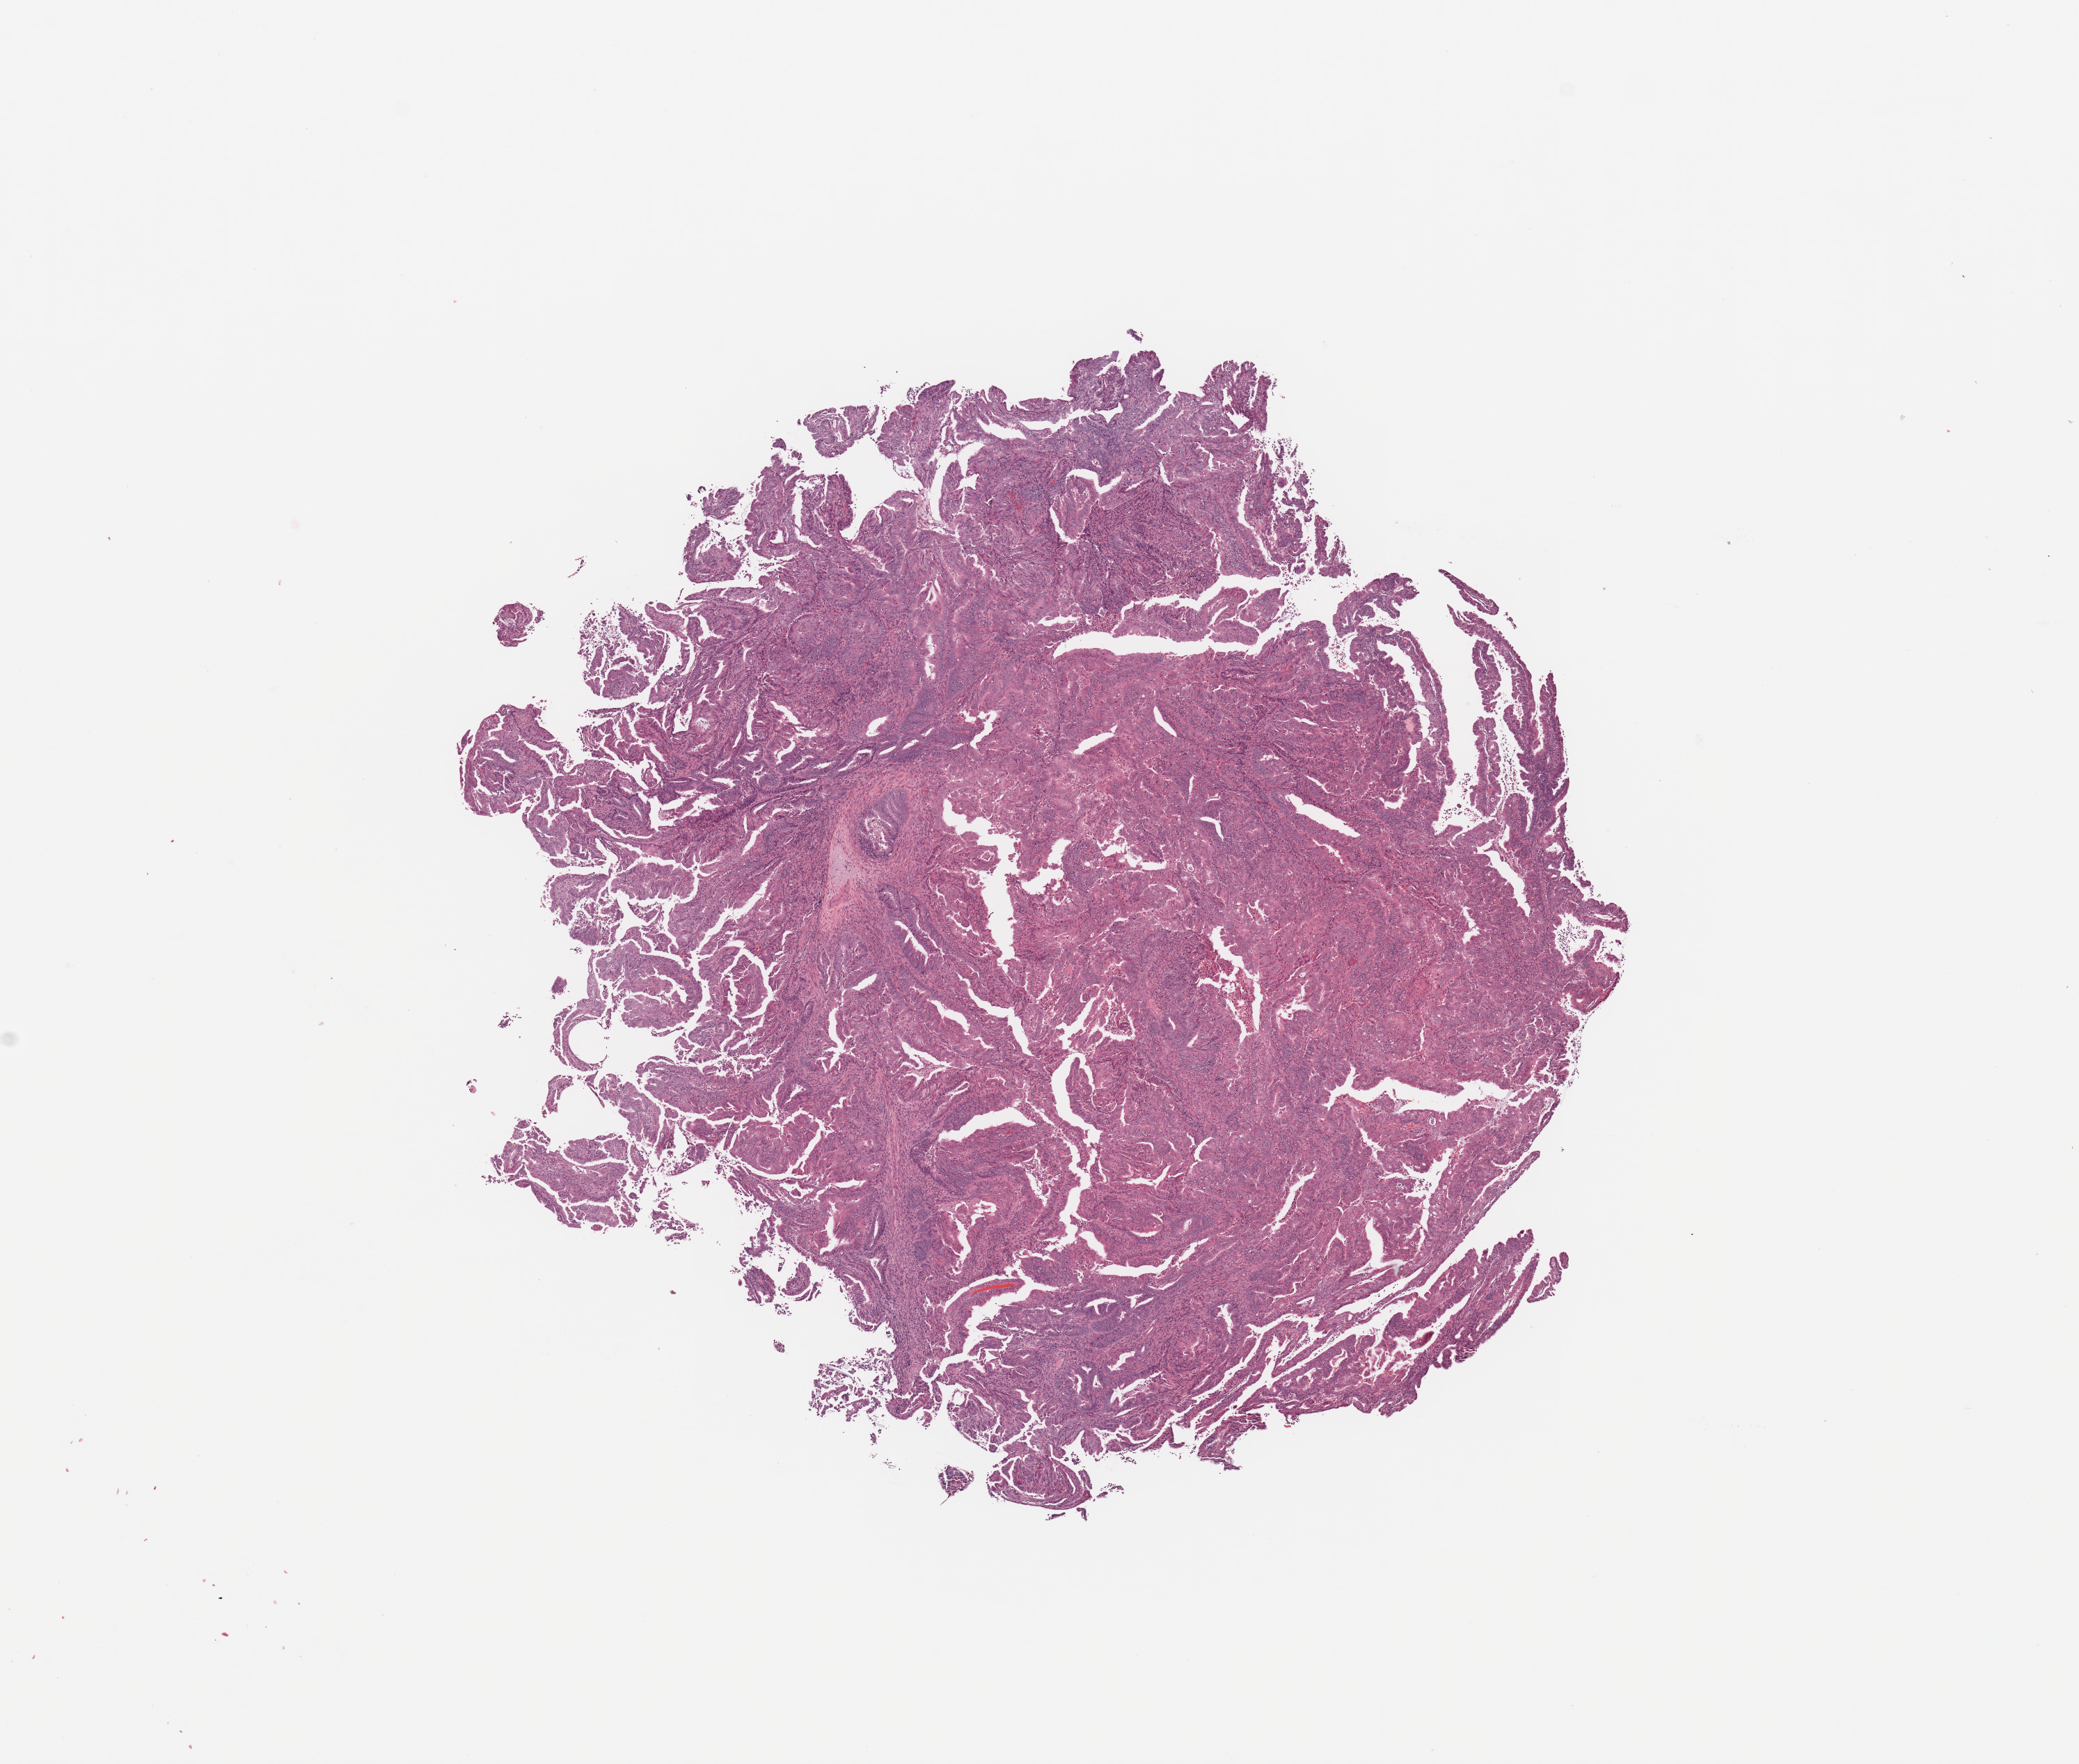
Whole-slide histology image, H&E-stained, shown as a low-resolution overview of the whole scanned area (about 11.8 x 10.0 mm, from a 20x scan); tumour tissue sample, sampled site: uterus. Female, 64 y/o. Histologic grade: G1 (well differentiated). Slide review estimates, as recorded: tumour nuclei 90%, necrosis 0%.
* diagnosis: Endometrioid adenocarcinoma, NOS
* AJCC pathologic stage: I
* primary tumour site (as recorded): posterior endometrium